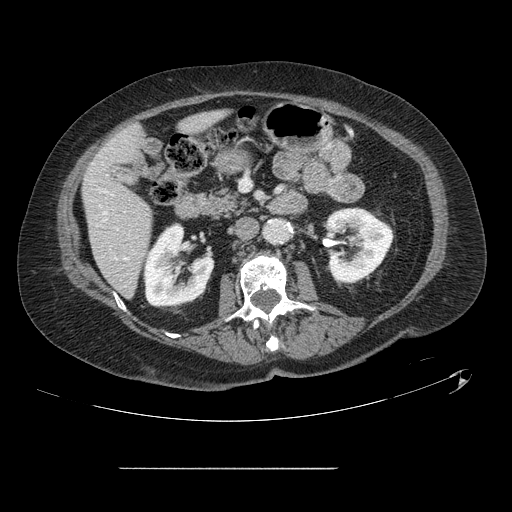
Contrast-enhanced abdominal CT, one axial slice. Position 42 of 148 along the scan axis. 120 kVp. Soft-tissue window (W 400 / L 40 HU). 2.5 mm slice thickness. 512 × 512 image matrix, field of view 439 × 439 mm. Female patient, age 75 years. Case-level facts recorded for this patient, not image findings: diagnosis: colorectal cancer liver metastases, imaged before liver resection; multiple liver metastases: no; largest metastasis: 2.4 cm.
Annotated regions visible in this slice (expert manual segmentation):
- hepatic veins: bounding box <104,212,127,260> (left, top, right, bottom; pixels)
- liver: <83,113,222,296>
- planned liver remnant (the part of the liver to remain after resection): <83,113,222,296>